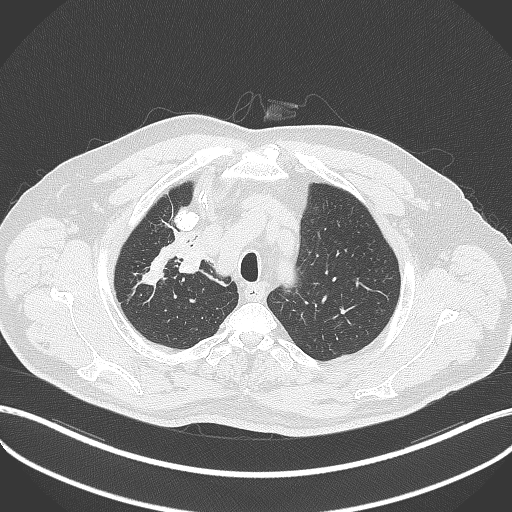
Chest CT, one axial slice. Position 319 of 411 along the scan axis. Reconstruction kernel B70f. Lung window (W 1500 / L -600 HU). 512 × 512 image matrix, field of view 400 × 400 mm. Patient: male, 60 years. Case-level facts recorded for this patient, not image findings: clinical TNM (as recorded): T1b N1 M0.
Structures marked on this image (bounding box drawn by a radiologist):
- lung tumour (recorded histology: squamous cell carcinoma): box from (x=174, y=232) to (x=212, y=279) px